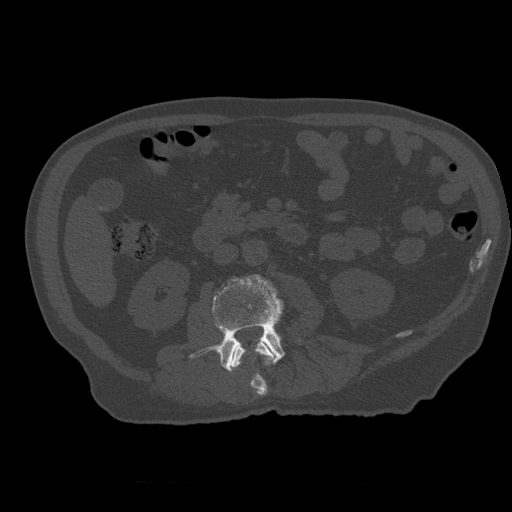
CT including the spine, one axial slice. Slice 197 of 399 in the series (ordered by position). Reconstruction kernel STANDARD. Bone window (W 1800 / L 400 HU). 1.25 mm slice thickness. 512 × 512 image matrix, field of view 407 × 407 mm. Patient age 73 years. From the clinical record (not read from this slice): primary cancer: prostate; vertebrae with lytic lesions (as recorded): L2.
Structures marked on this image (semi-automatic segmentation, software-assisted and operator-edited):
- L2 vertebra: bounding box [x1, y1, x2, y2] px = [230, 341, 274, 396]
- L3 vertebra: [190, 275, 285, 372]